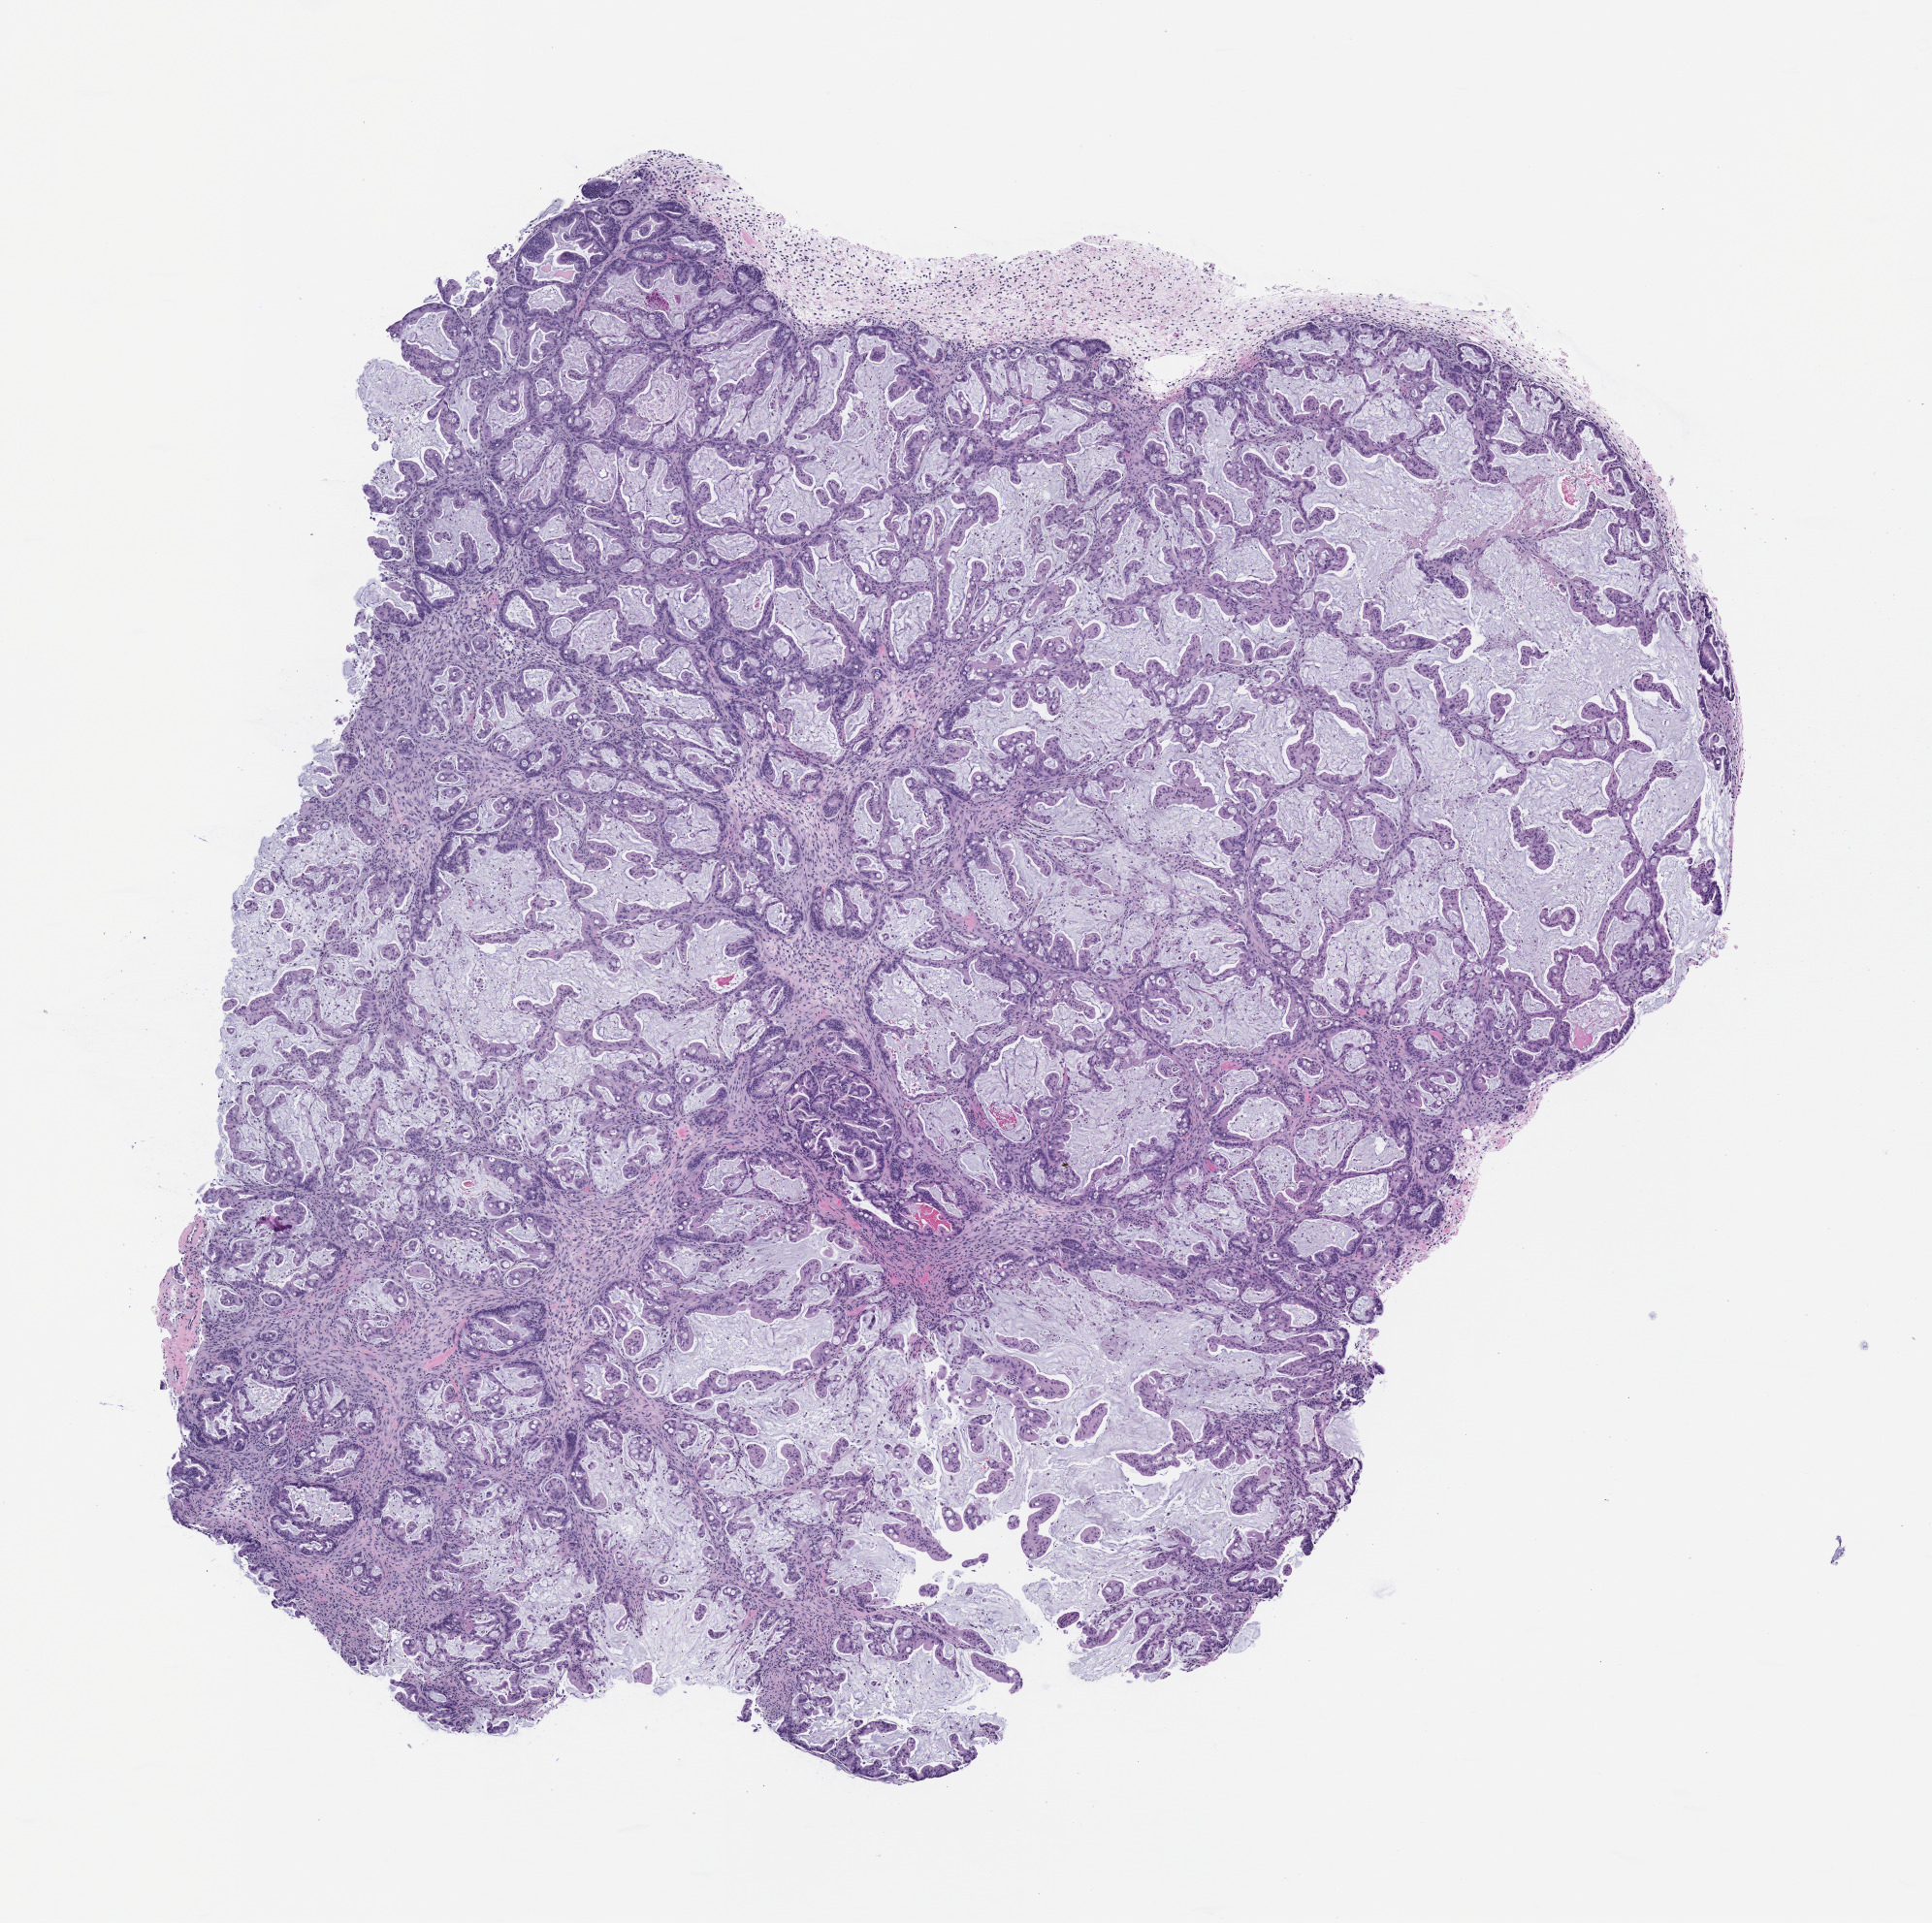
Haematoxylin and eosin whole-slide image of a patient-derived xenograft (PDX) tumor grown in a mouse, passage 1, a low-resolution overview of the entire scanned area, about 8.0 x 8.0 mm; formalin-fixed paraffin-embedded section; originating tumor site category: rectum.
Originating patient diagnosis: Rectal Adenocarcinoma.